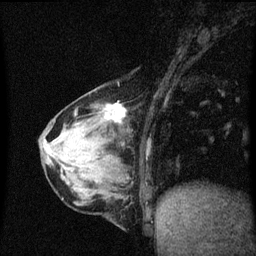
Breast MRI (dynamic contrast-enhanced), one sagittal slice. Slice 18 of 60 in the series (ordered by position). Dynamic contrast-enhanced series, image 2 of 3 at this slice position (ordered by acquisition). 1.5 T. TE 4.2 ms, TR 8.4 ms. 256 × 256 image matrix. Patient: female, 64 years. From the clinical record (not read from this slice): setting: breast cancer imaged before/during neoadjuvant chemotherapy; receptor status: HR-positive, HER2-negative.
Structures marked on this image (semi-automatic segmentation, software-assisted and operator-edited):
- analysis volume of interest (the breast-tissue region the enhancement analysis was run in; not a lesion): bounding box (x1, y1, x2, y2) in pixels: (65, 96, 127, 157)
- tumour enhancement mask (voxels above the 70 % enhancement threshold inside the analysis volume of interest): (109, 104, 126, 119)